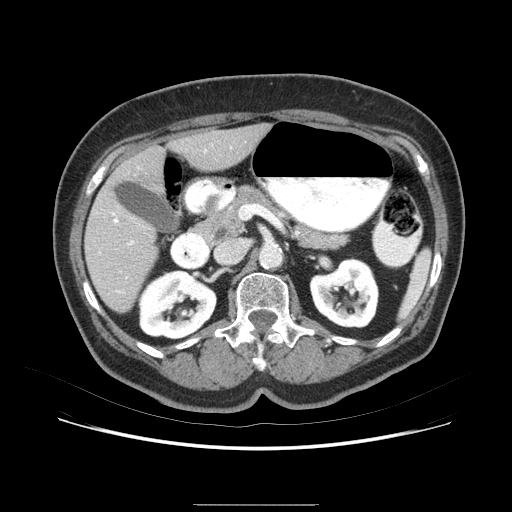
Contrast-enhanced abdominal CT (liver protocol), one axial slice. Slice 34 of 79 in the series (ordered by position). 120 kVp. Soft-tissue window (W 400 / L 40 HU). 2.5 mm slice thickness. 512 × 512 image matrix, field of view 380 × 380 mm. Case-level facts recorded for this patient, not image findings: diagnosis: hepatocellular carcinoma (patient treated with transarterial chemoembolisation; whether this scan precedes or follows treatment is not stated here); TNM stage (as recorded): Stage-I; Child-Pugh class: A; tumour nodularity: uninodular.
Annotated regions visible in this slice (semi-automatic segmentation, software-assisted and operator-edited):
- liver parenchyma outside the tumour (the mass and vessels are separate outlines, so this box may not span the whole liver): bounding box [x1, y1, x2, y2] px = [84, 121, 276, 324]
- mass: [106, 199, 151, 231]
- liver vessels: [98, 150, 237, 285]